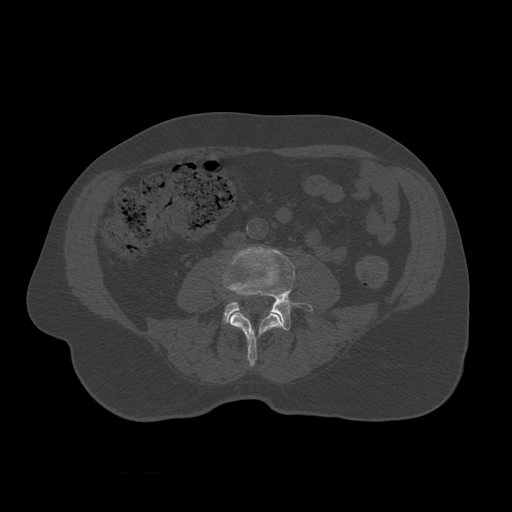
CT including the spine, one axial slice. Slice 288 of 450 in the series (ordered by position). Bone window (W 1800 / L 400 HU). 1.25 mm slice thickness. 512 × 512 image matrix, field of view 405 × 405 mm. Patient age 75 years. From the clinical record (not read from this slice): primary cancer: prostate.
Structures marked on this image (semi-automatic segmentation, software-assisted and operator-edited):
- L3 vertebra: bounding box (x1, y1, x2, y2) in pixels: (230, 311, 283, 368)
- L4 vertebra: (223, 247, 313, 331)